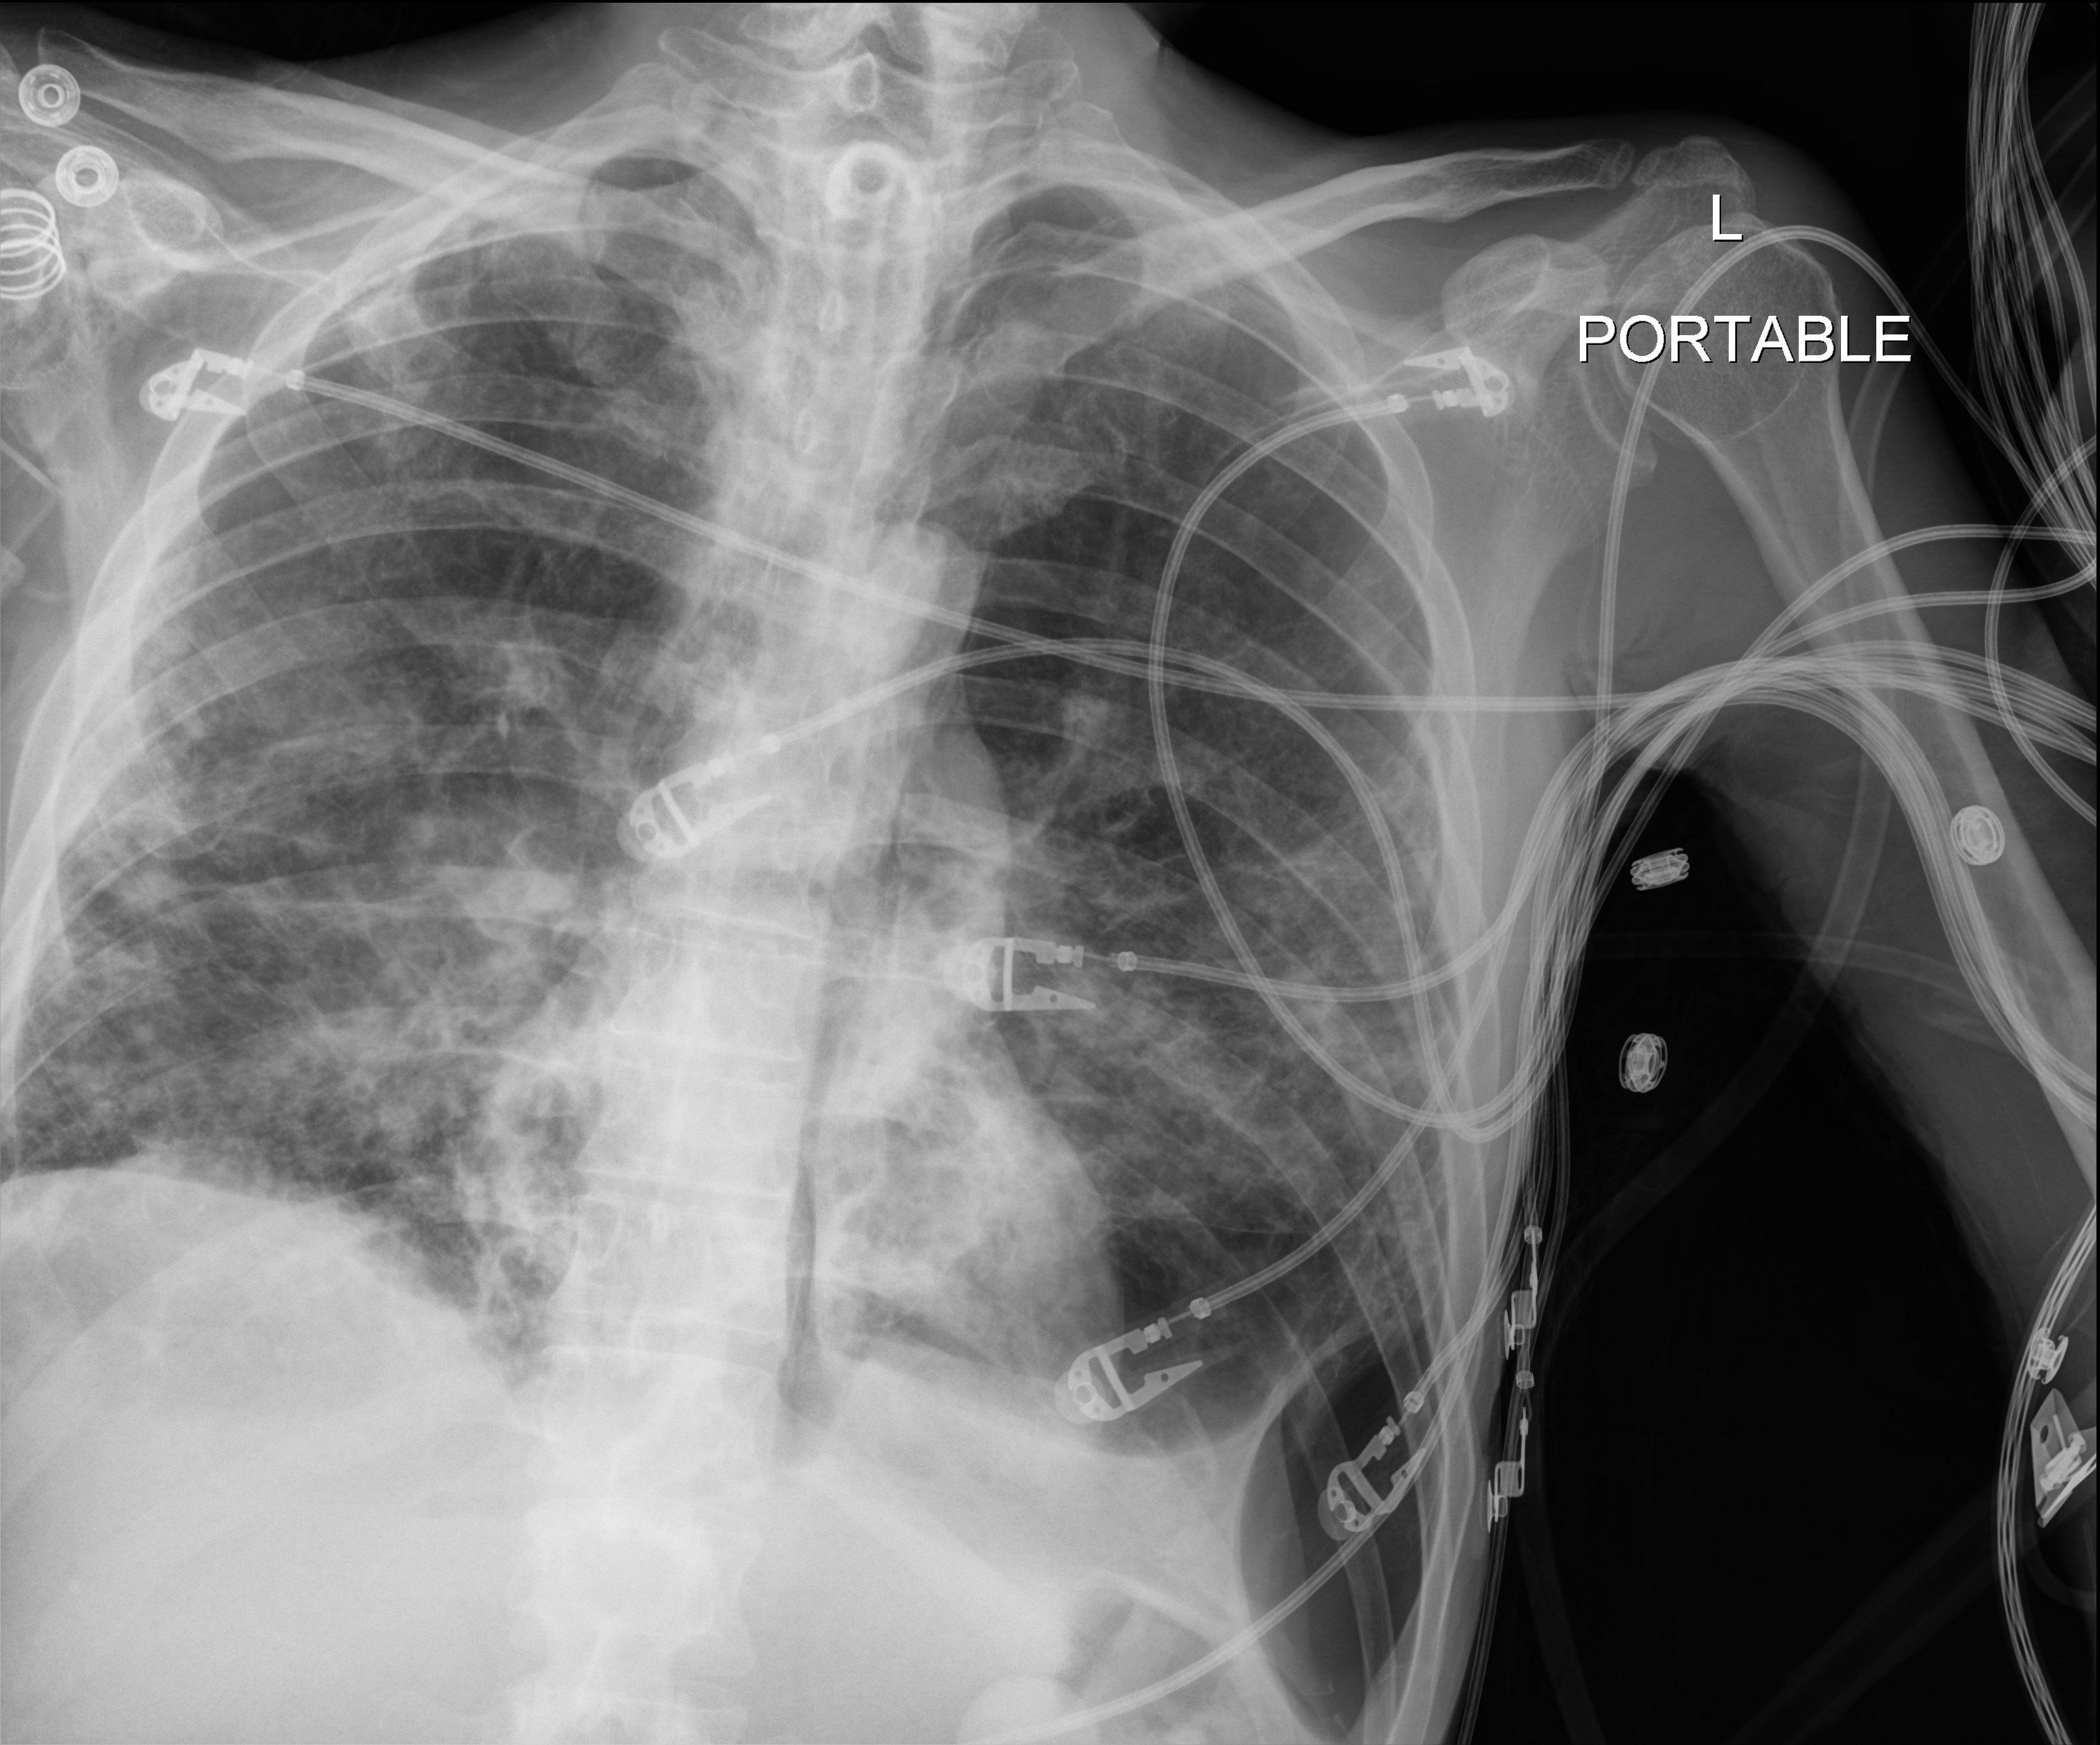
Chest X-ray, anteroposterior (AP) projection. Patient hospitalised with COVID-19; male, aged 18–59 years.
From the hospital-stay record, not from the radiograph (when in the stay this image was taken is not recorded): mechanically ventilated during this hospital stay: yes; hypertension (admission record): yes.